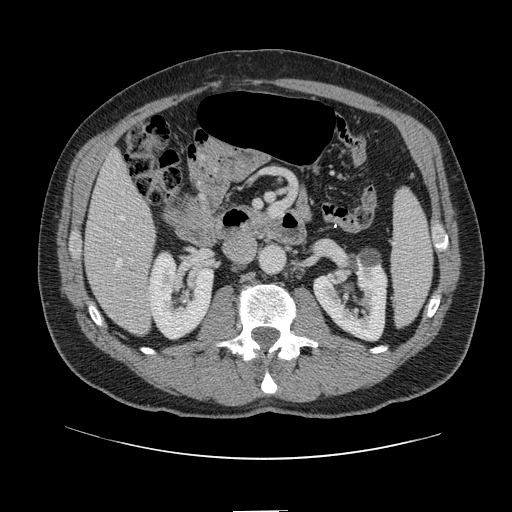
Contrast-enhanced abdominal CT, one axial slice. Position 41 of 161 along the scan axis. Intravenous contrast given. Soft-tissue window (W 400 / L 40 HU). 512 × 512 image matrix, field of view 412 × 412 mm. Male patient, age 66 years. From the clinical record (not read from this slice): diagnosis: colorectal cancer liver metastases, imaged before liver resection; multiple liver metastases: no; largest metastasis: 3.5 cm; chemotherapy before resection: yes.
Structures marked on this image (outlined manually by an expert reader):
- hepatic veins: bounding box <117,216,124,266> (left, top, right, bottom; pixels)
- liver: <86,154,155,335>
- planned liver remnant (the part of the liver to remain after resection): <86,154,152,270>